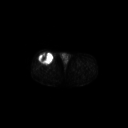
FDG PET of an extremity soft-tissue mass (from a PET/CT study), one axial slice. Position 278 of 311 along the scan axis. 3.27 mm slice thickness. 128 × 128 image matrix. Male patient, age 56 years. Case-level facts recorded for this patient, not image findings: histological type: pleiomorphic leiomyosarcoma; grade: intermediate; site of the primary tumour: right thigh.
Annotated regions visible in this slice (expert contour drawn on MRI and transferred to this co-registered scan by the dataset authors):
- gross tumour volume including surrounding oedema: bounding box [x1, y1, x2, y2] px = [38, 52, 54, 65]
- gross tumour volume (mass): [38, 52, 54, 65]